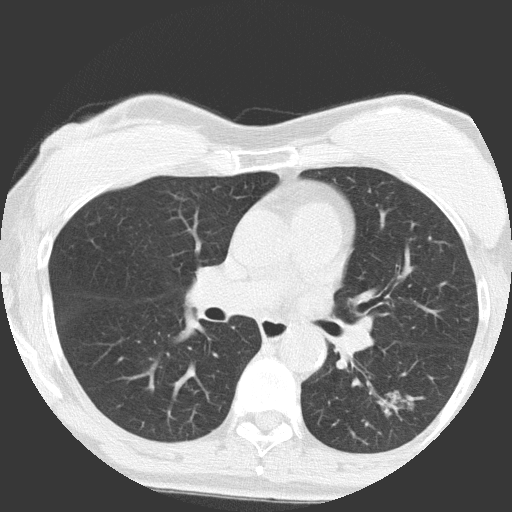
Chest CT (low-dose screening protocol), one axial image; first (baseline) screen; lung window (W 1500 / L -600 HU); 2 mm slice thickness; slice 65 of 149 in the series. Female, age 64 years at enrolment. Former smoker at enrolment.
Lesion marked by an expert reader, bounding box (x1, y1, x2, y2) in pixels: (355, 375, 439, 450). Reader record for this screening exam (exam-level; its link to the box is not recorded): non-calcified nodule or mass ≥4 mm, right upper lobe, 4 × 4 mm, poorly defined margins, ground glass attenuation. Note: the box lies in the patient's left hemithorax on this image, whereas the reader's record names the right lung; they may be different findings. Participant outcome: lung cancer diagnosed 932 days after this screen (after the third annual screen) — adenocarcinoma, NOS, left lower lobe, moderately differentiated (G2), stage IA (AJCC 6th edition), 17 mm at pathology.